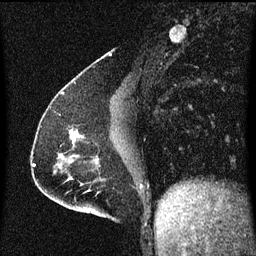
Breast MRI (dynamic contrast-enhanced), one sagittal slice; position 23 of 60 along the scan axis; dynamic contrast-enhanced series, image 2 of 3 at this slice position (ordered by acquisition); 1.5 T; TE 4.2 ms, TR 8 ms; 2 mm slice thickness; 256 × 256 image matrix. Patient: female, 51 years.
Annotated regions visible in this slice (semi-automatically segmented with operator editing):
- analysis volume of interest (the breast-tissue region the enhancement analysis was run in; not a lesion): bounding box [x1, y1, x2, y2] px = [70, 128, 89, 149]
- tumour enhancement mask (voxels above the 70 % enhancement threshold inside the analysis volume of interest): [70, 130, 81, 143]